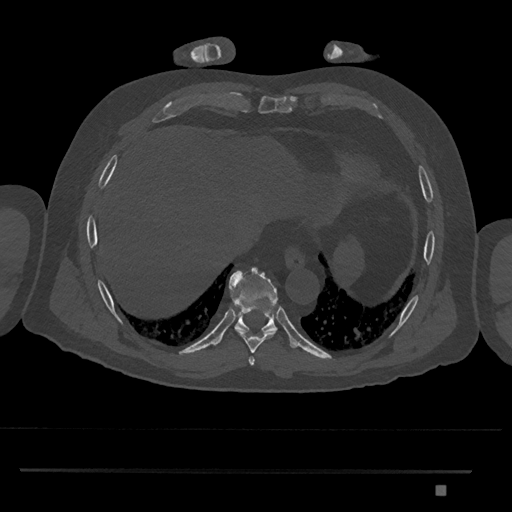
CT including the spine, one axial slice. Position 1084 of 1134 along the scan axis. Reconstruction kernel Br40s/3. Bone window (W 1800 / L 400 HU). 0.5 mm slice thickness. 512 × 512 image matrix, field of view 429 × 429 mm. Male patient, age 65 years. From the clinical record (not read from this slice): primary cancer: prostate.
Annotated regions visible in this slice (semi-automatic segmentation, software-assisted and operator-edited):
- T8 vertebra: box from (x=235, y=329) to (x=276, y=354) px
- T9 vertebra: (x=229, y=267)–(x=278, y=334)